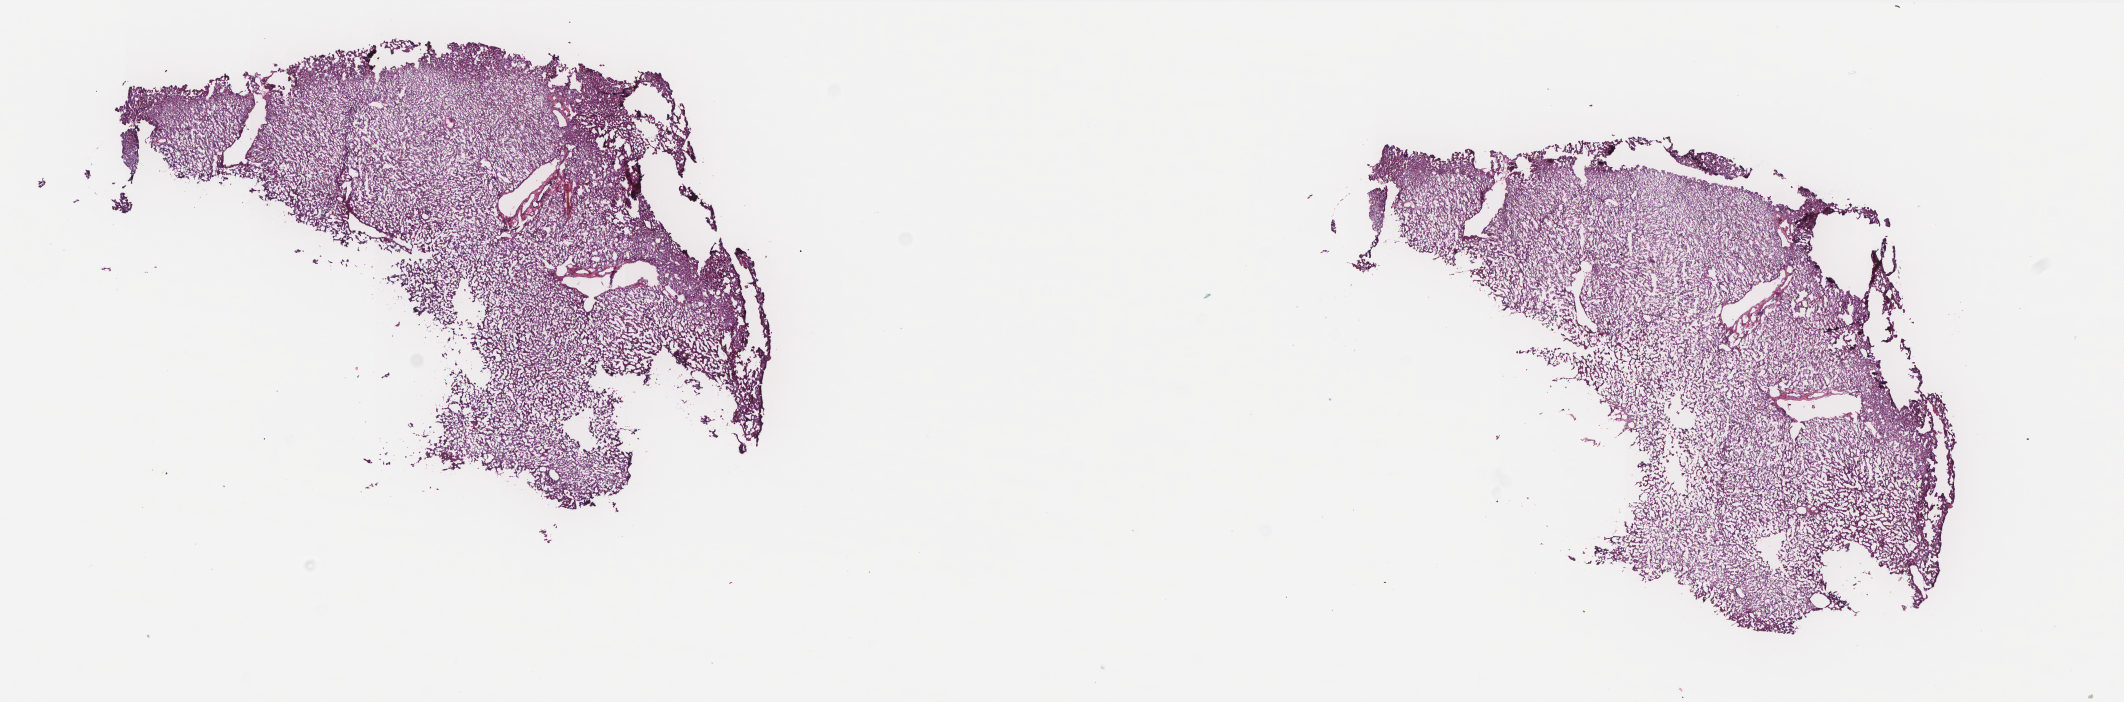
H&E-stained whole-slide image — whole scanned area (about 17.0 x 5.6 mm, from a 20x scan) shown as a low-resolution overview. Frozen section from the top of the tissue portion. Sample: solid tissue normal (non-tumour tissue), liver. Patient: female, age at initial diagnosis 72 years. Pathologist review of this section (percent, as recorded): tumour cells 0%, tumour nuclei 0%, normal cells 100%, stromal cells 0%, necrosis 0%. Infiltration values recorded for this section: lymphocyte infiltration 1%, monocyte infiltration 0%, neutrophil infiltration 0%.
* this section: solid tissue normal sample (biorepository sample class)
* patient diagnosis: Hepatocellular carcinoma, NOS